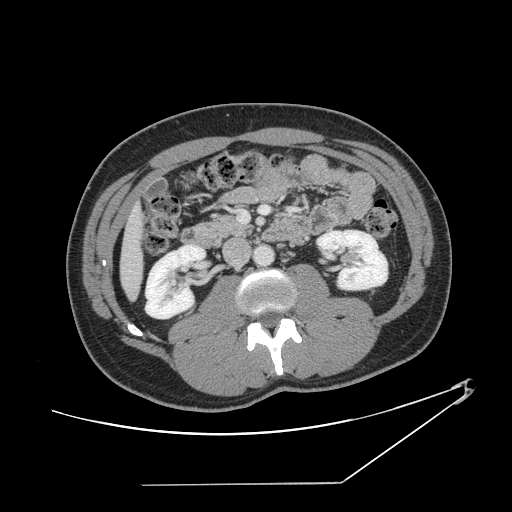
Contrast-enhanced abdominal CT, one axial slice; position 48 of 152 along the scan axis; reconstruction kernel STANDARD; 120 kVp; soft-tissue window (W 400 / L 40 HU); 512 × 512 image matrix, field of view 432 × 432 mm. Male patient, age 45 years. From the clinical record (not read from this slice): diagnosis: colorectal cancer liver metastases, imaged before liver resection; multiple liver metastases: no; largest metastasis: 1 cm; chemotherapy before resection: yes.
Annotated regions visible in this slice (manually delineated by an expert):
- liver: bounding box [x1, y1, x2, y2] px = [122, 211, 143, 296]
- planned liver remnant (the part of the liver to remain after resection): [121, 212, 143, 296]
- portal vein (with intrahepatic branches): [240, 206, 269, 222]